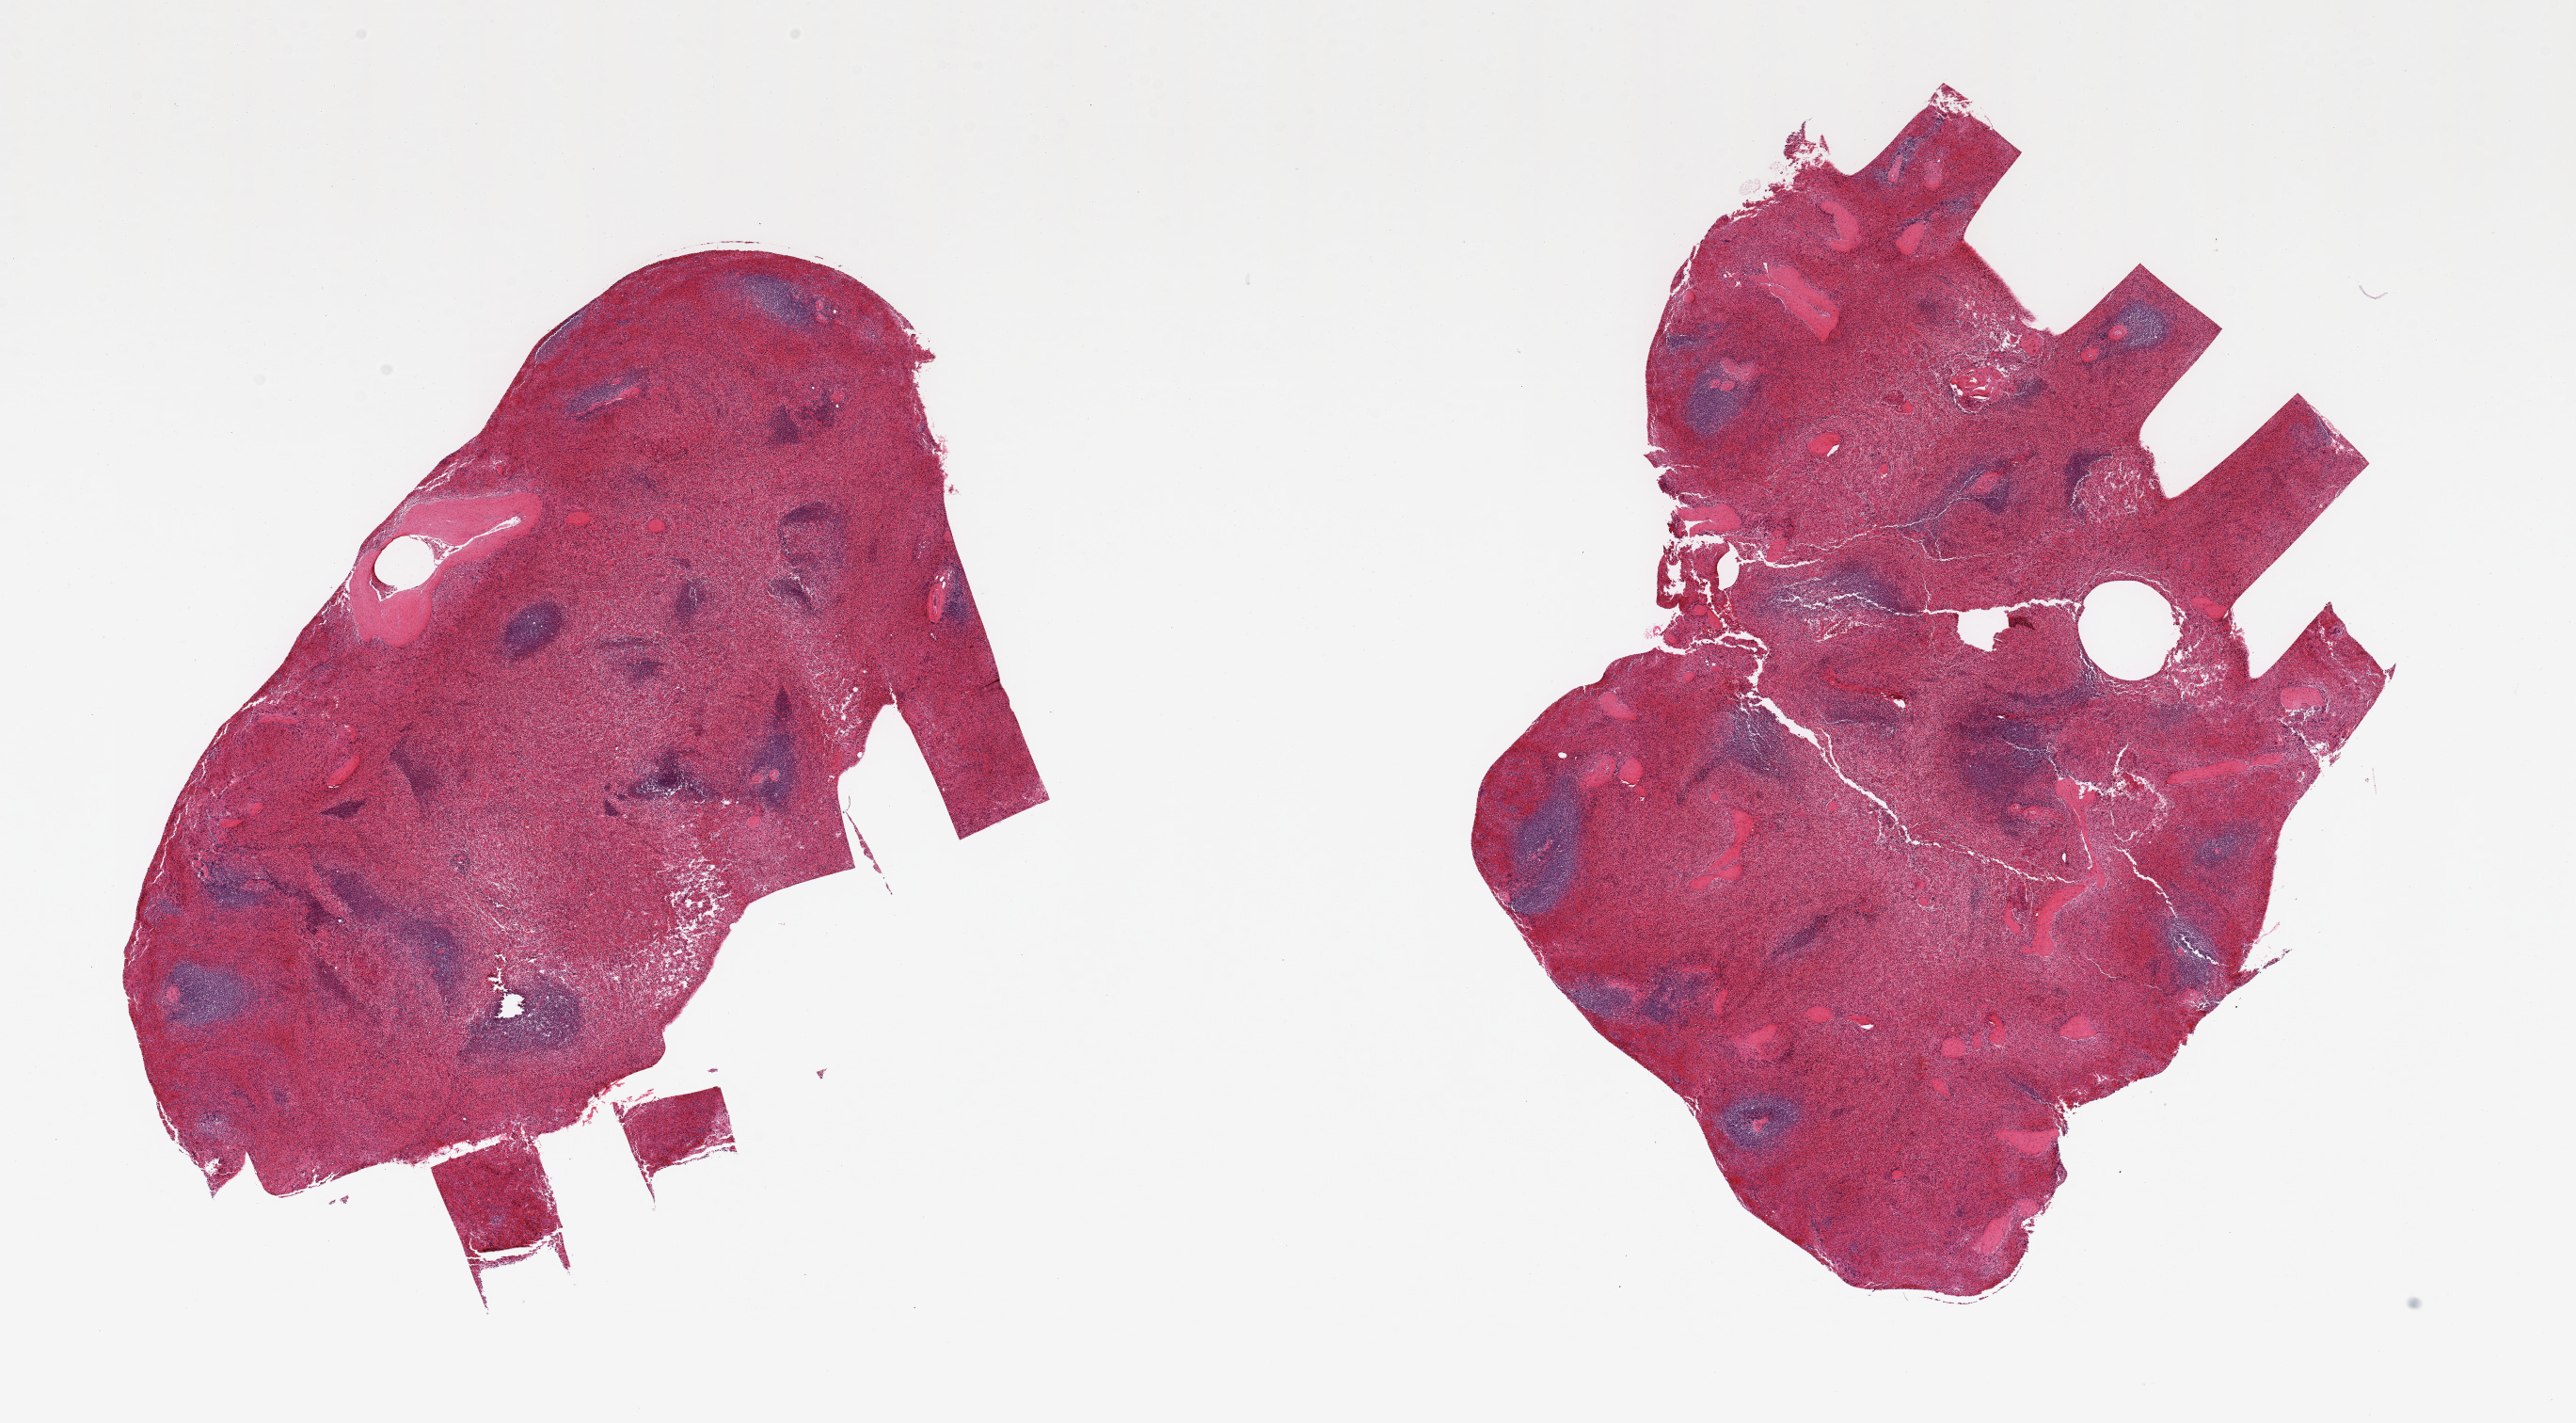
Whole-slide image, hematoxylin and eosin (H&E) stain, shown as a low-resolution overview of the whole scanned area (about 21.7 x 12.0 mm), PAXgene-fixed, paraffin-embedded tissue, sampled site (target tissue): spleen, donor tissue sample. Donor sex: male.
Reviewer comment on this tissue sample: 2 pieces, moderate congestion.